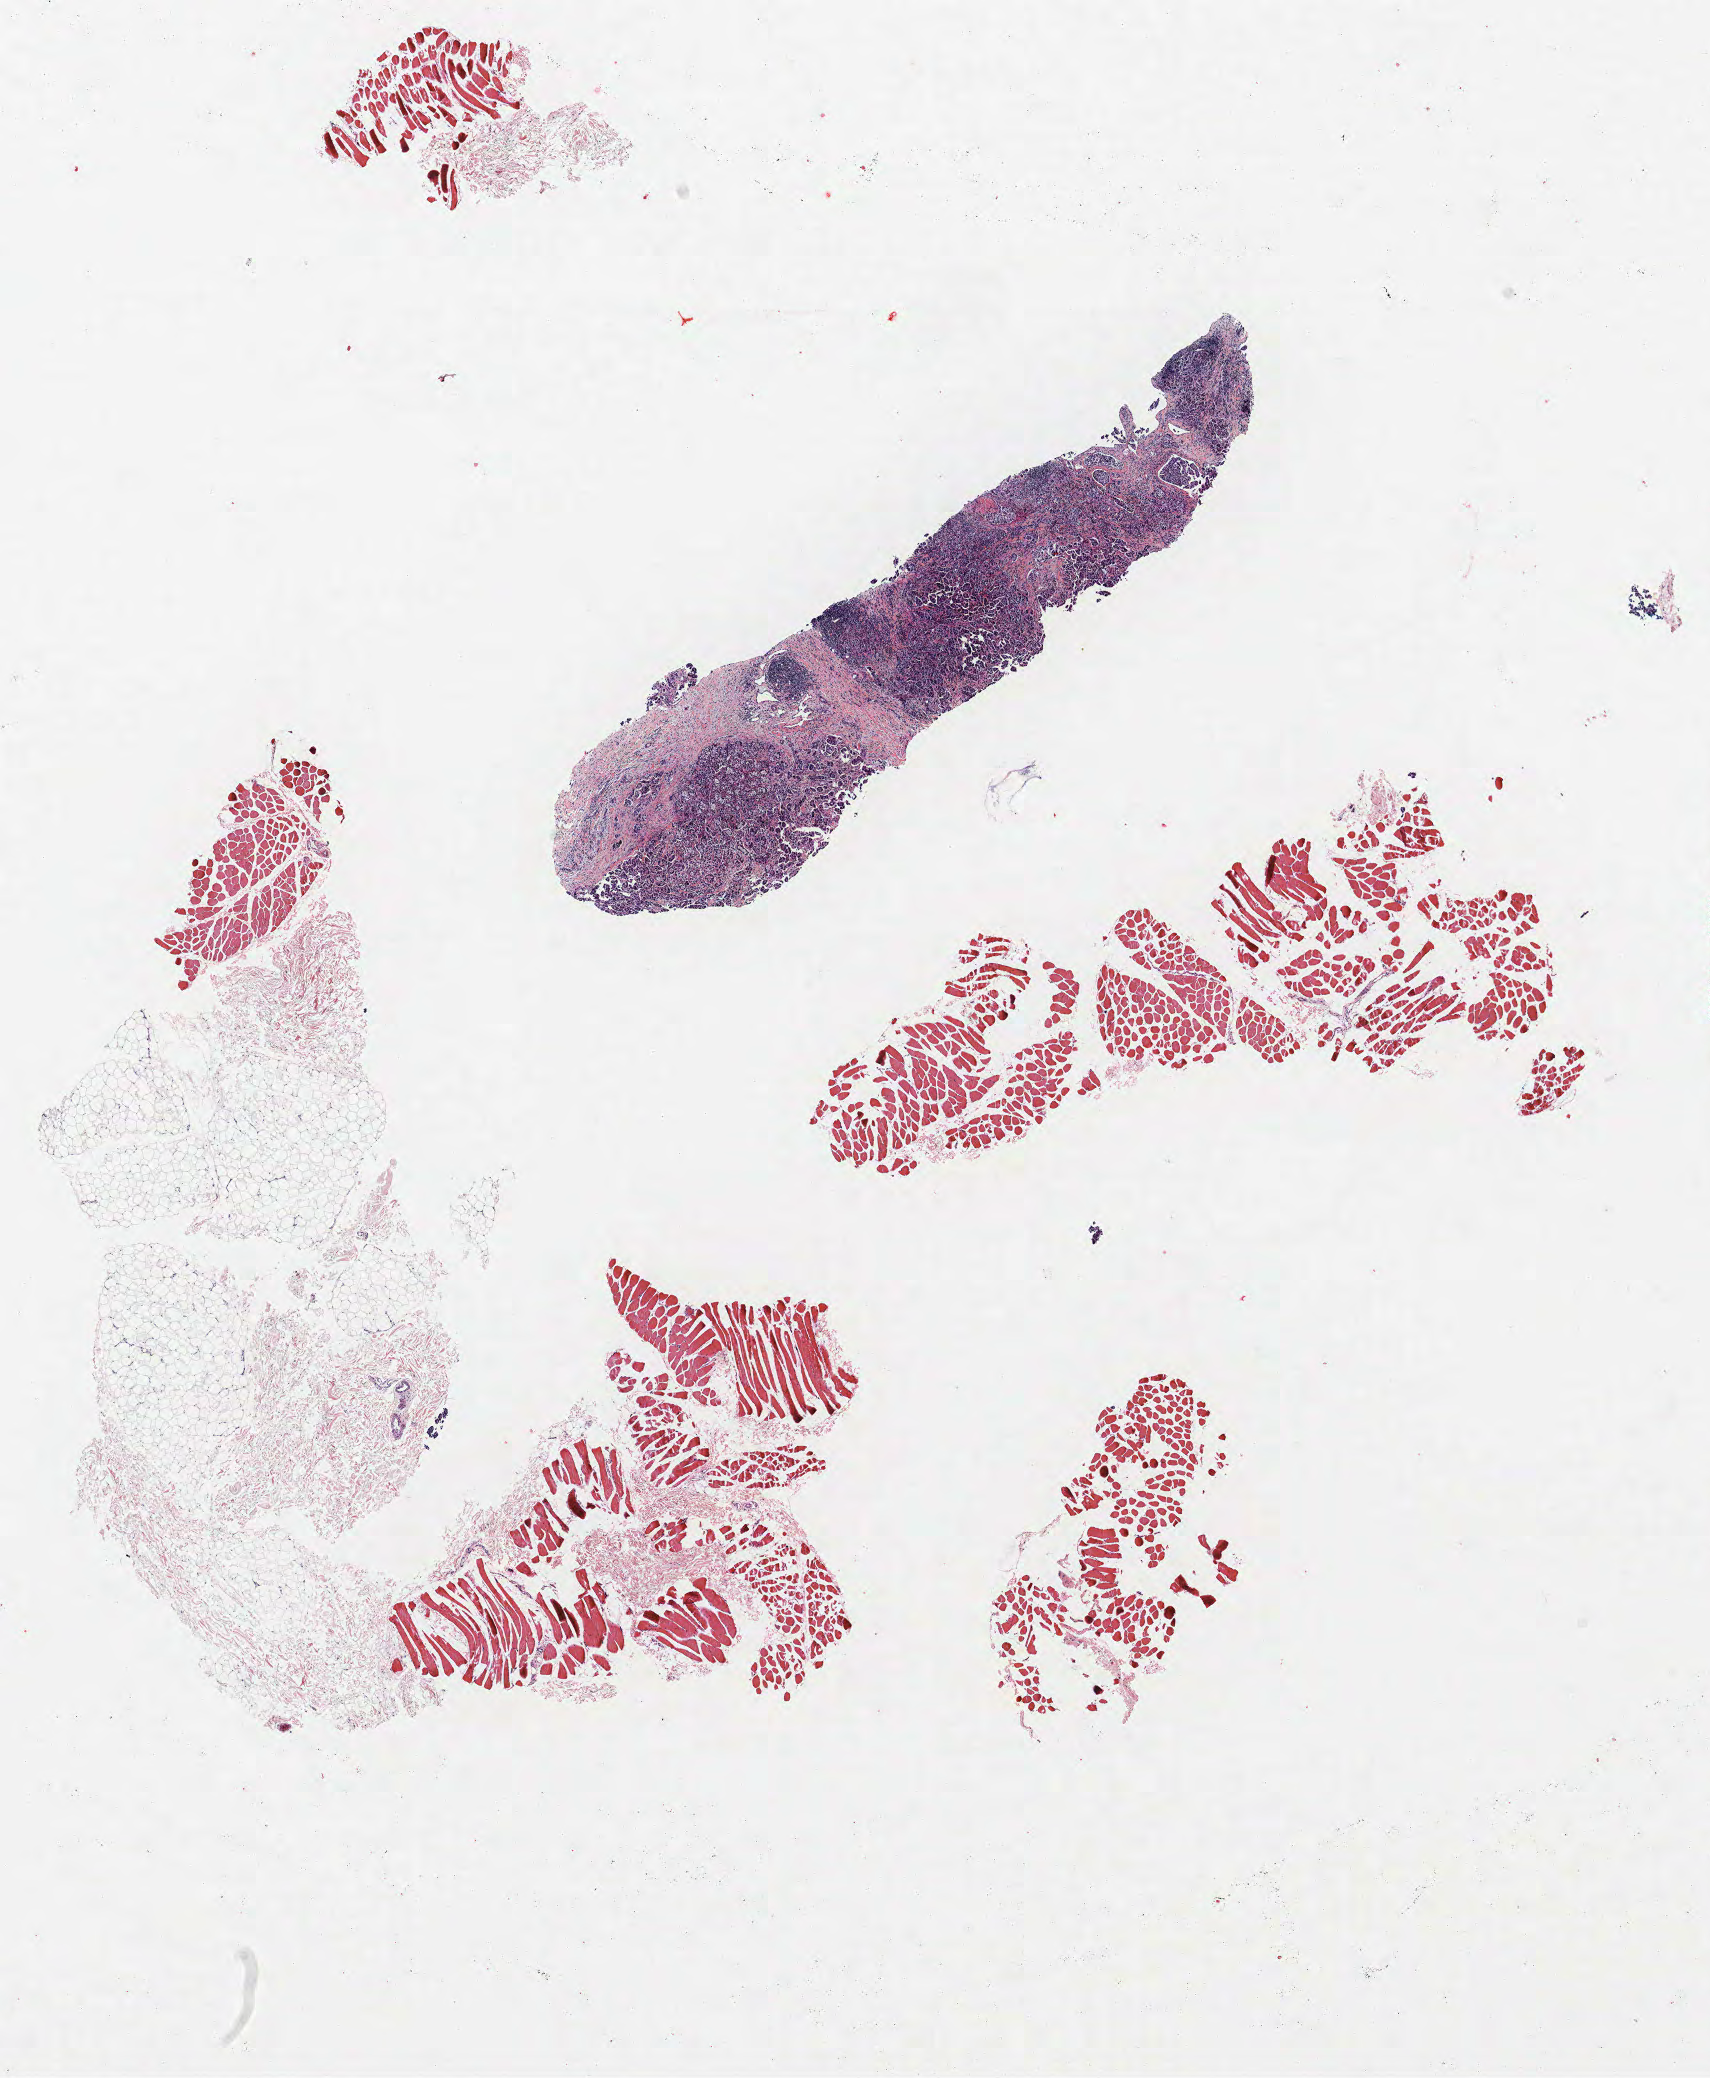
Whole-slide histology image, Hematoxylin and eosin (H&E) stained, low-resolution overview of the scanned area, about 13.7 x 16.6 mm; formalin-fixed paraffin-embedded (FFPE) section; lung tissue. Male, age 72 at enrolment. Former smoker at enrolment.
Tumour size (pathology): 27 mm. Stage (AJCC 6th edition): IIIB. Primary tumour location (clinical record): right middle lobe. Participant's lung-cancer diagnosis: Adenocarcinoma, NOS.